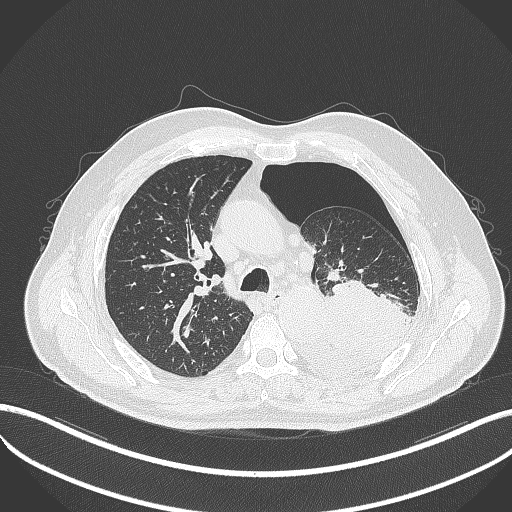
Chest CT, one axial slice. Position 352 of 464 along the scan axis. Reconstruction kernel B70f. 120 kVp. Lung window (W 1500 / L -600 HU). 512 × 512 image matrix, field of view 400 × 400 mm. Male patient, age 76 years. From the clinical record (not read from this slice): clinical TNM (as recorded): T3 N0 M1b.
Structures marked on this image (bounding box drawn by a radiologist):
- lung tumour (recorded histology: adenocarcinoma): box from (x=326, y=276) to (x=412, y=350) px